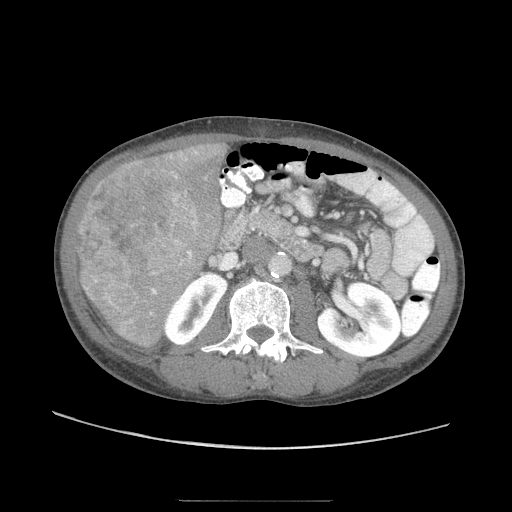
Contrast-enhanced abdominal CT (liver protocol), one axial slice. Slice 23 of 103 in the series (ordered by position). Reconstruction kernel STANDARD. 120 kVp. Soft-tissue window (W 400 / L 40 HU). 2.5 mm slice thickness. 512 × 512 image matrix, field of view 380 × 380 mm. Case-level facts recorded for this patient, not image findings: diagnosis: hepatocellular carcinoma (patient treated with transarterial chemoembolisation; whether this scan precedes or follows treatment is not stated here); TNM stage (as recorded): Stage-IIIA; Child-Pugh class: A; tumour differentiation: moderately differentiated; tumour nodularity: multinodular.
Structures marked on this image (semi-automatic segmentation, software-assisted and operator-edited):
- liver parenchyma outside the tumour (the mass and vessels are separate outlines, so this box may not span the whole liver): bounding box <80,138,230,348> (left, top, right, bottom; pixels)
- mass: <75,158,202,316>